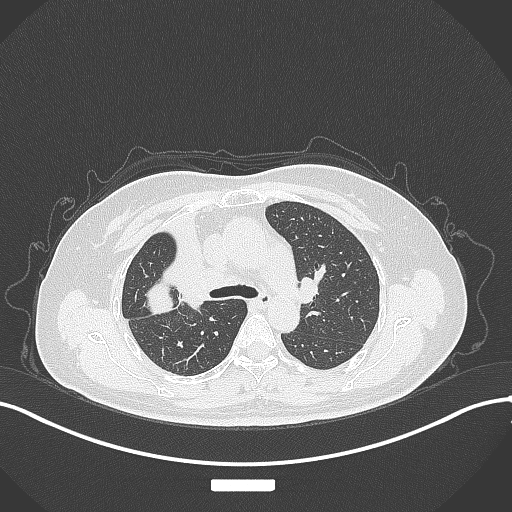
Chest CT, one axial slice; position 208 of 309 along the scan axis; 120 kVp; lung window (W 1500 / L -600 HU); 1 mm slice thickness; 512 × 512 image matrix. Patient: female, 60 years. From the clinical record (not read from this slice): clinical TNM (as recorded): T3 N1 M1.
Structures marked on this image (rectangle marked by the reading radiologist):
- lung tumour (recorded histology: adenocarcinoma): bounding box <137,279,187,321> (left, top, right, bottom; pixels)